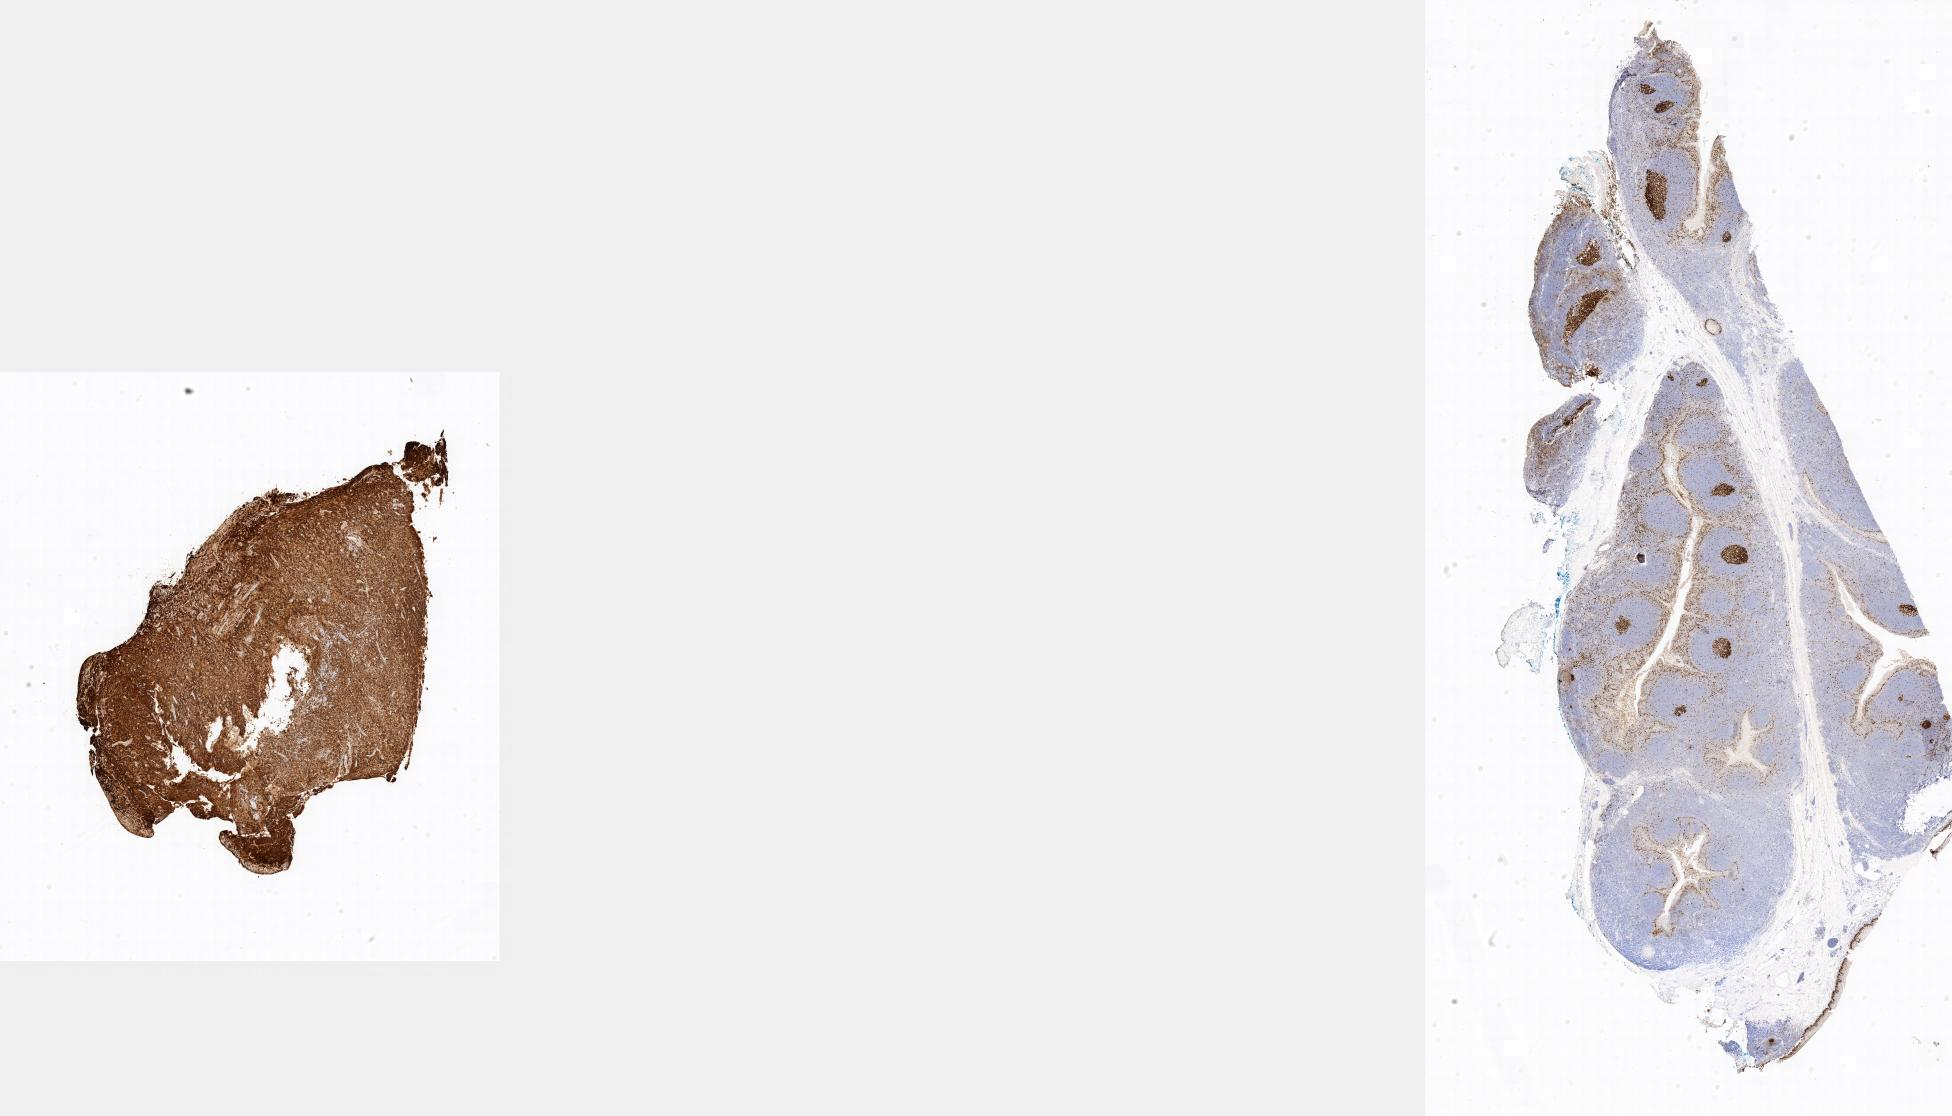
Whole-slide image, immunohistochemical stain for Ki-67 — whole scanned area shown as a low-resolution overview; tumor tissue; anatomic site: ovary. Patient: female, age at initial diagnosis 3 years.
Histologic diagnosis: Burkitt lymphoma, NOS.